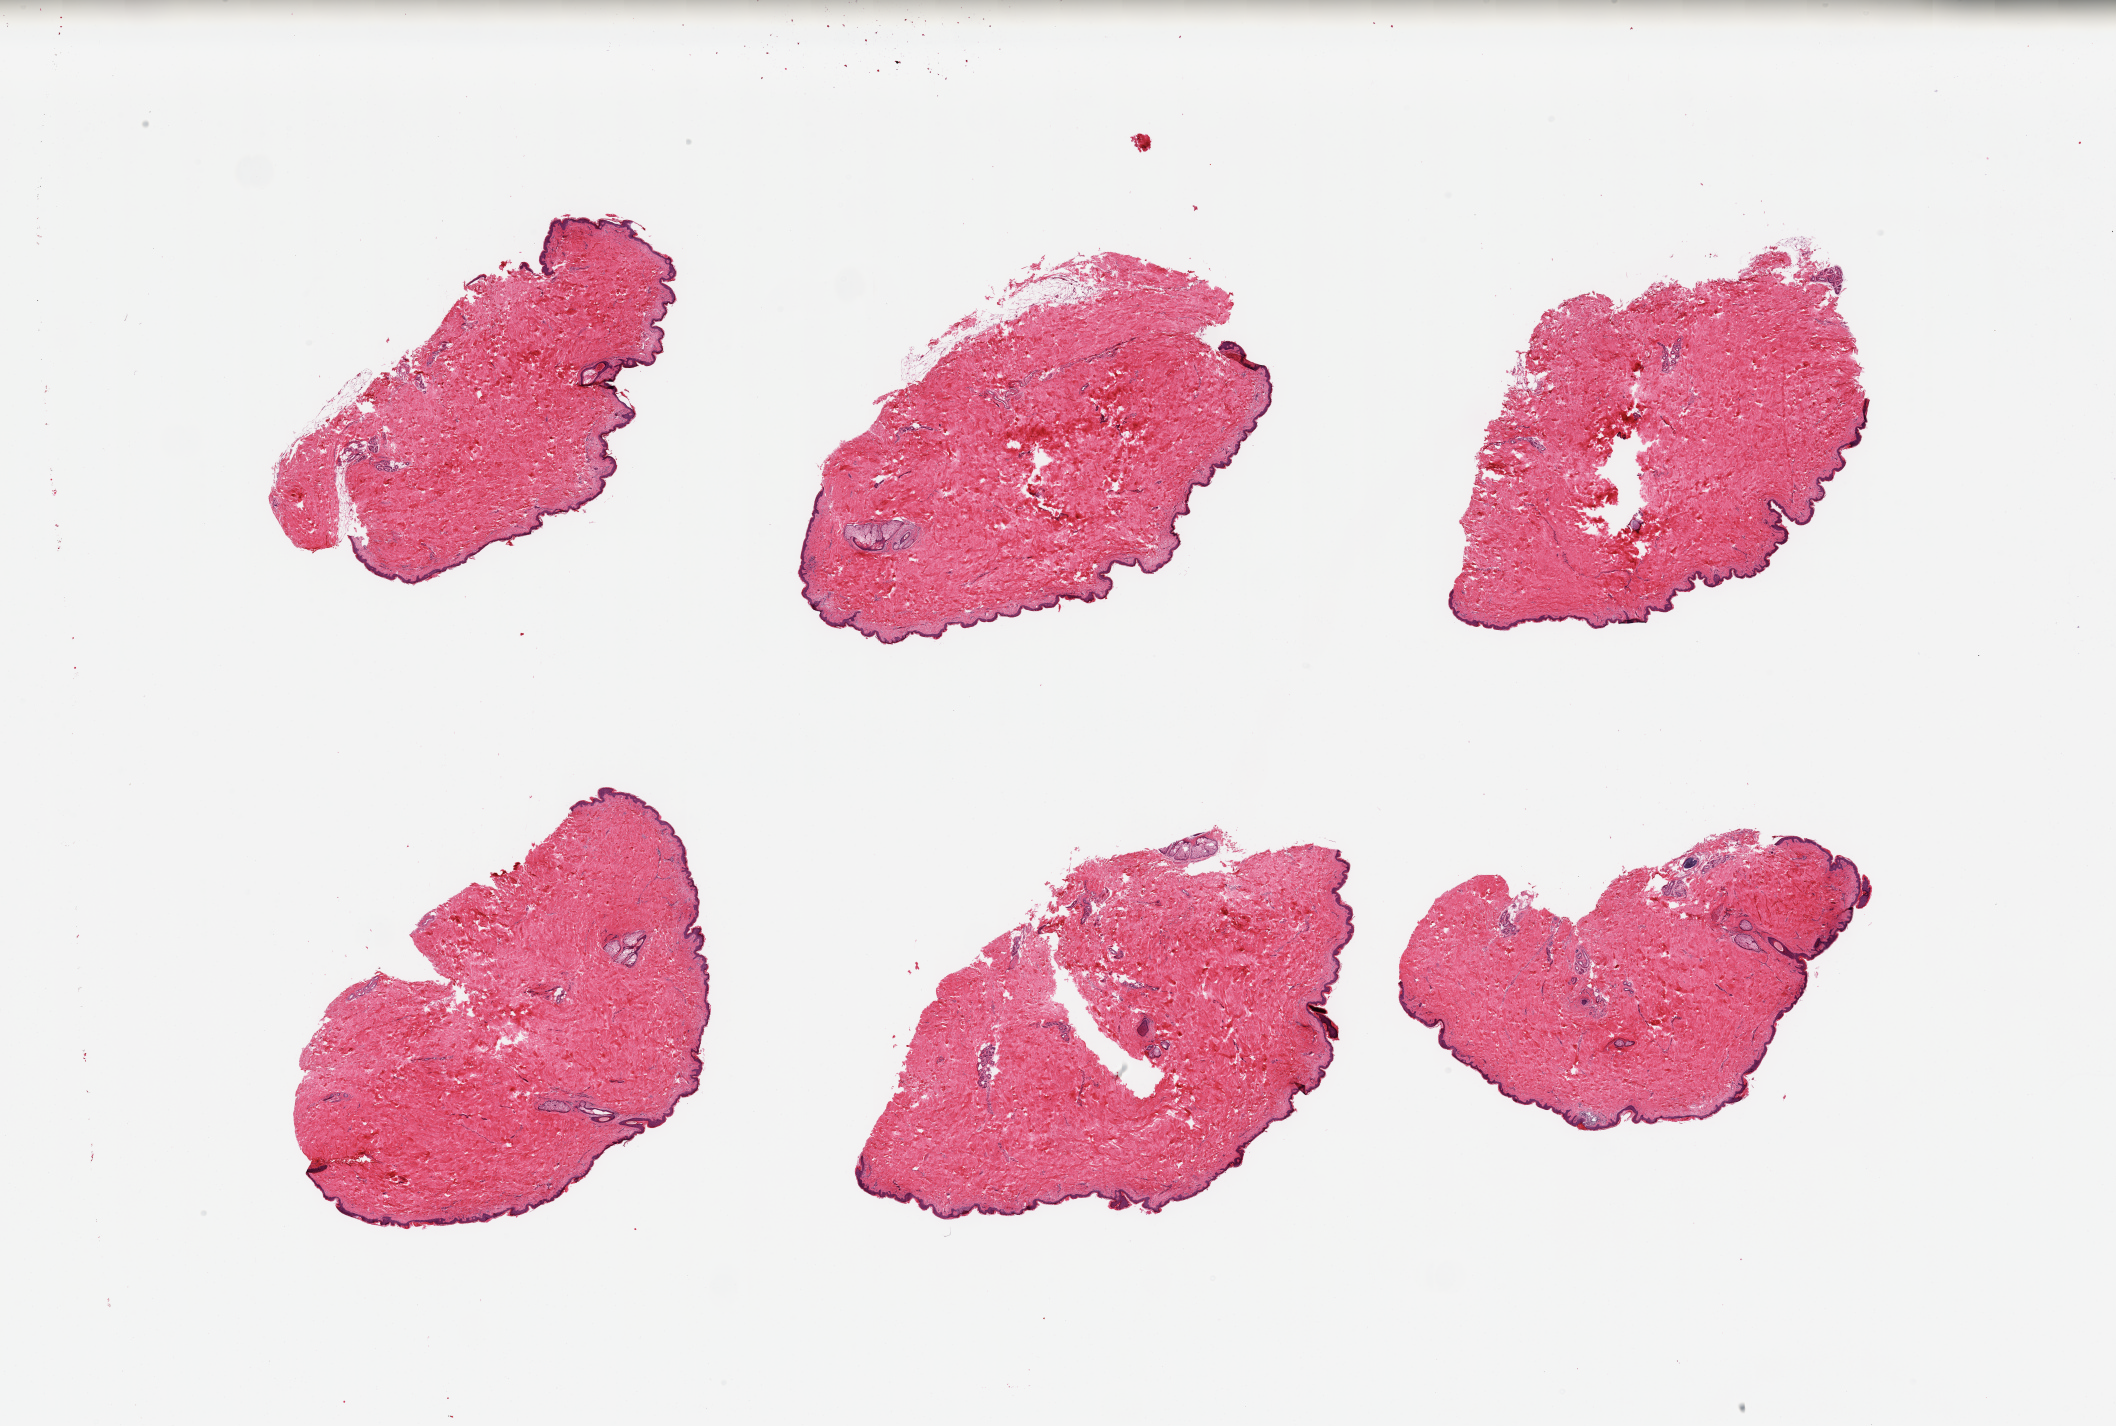
Hematoxylin and eosin (H&E) whole-slide image — shown as a low-resolution overview of the whole scanned area (about 33.5 x 22.6 mm, from a 20x scan), PAXgene-fixed paraffin-embedded (PFPE) section, sampled site (target tissue): skin of suprapubic region, donor tissue sample. Donor: male.
Review note (as recorded): 6 pieces; well dissected; <2% dermal fat.